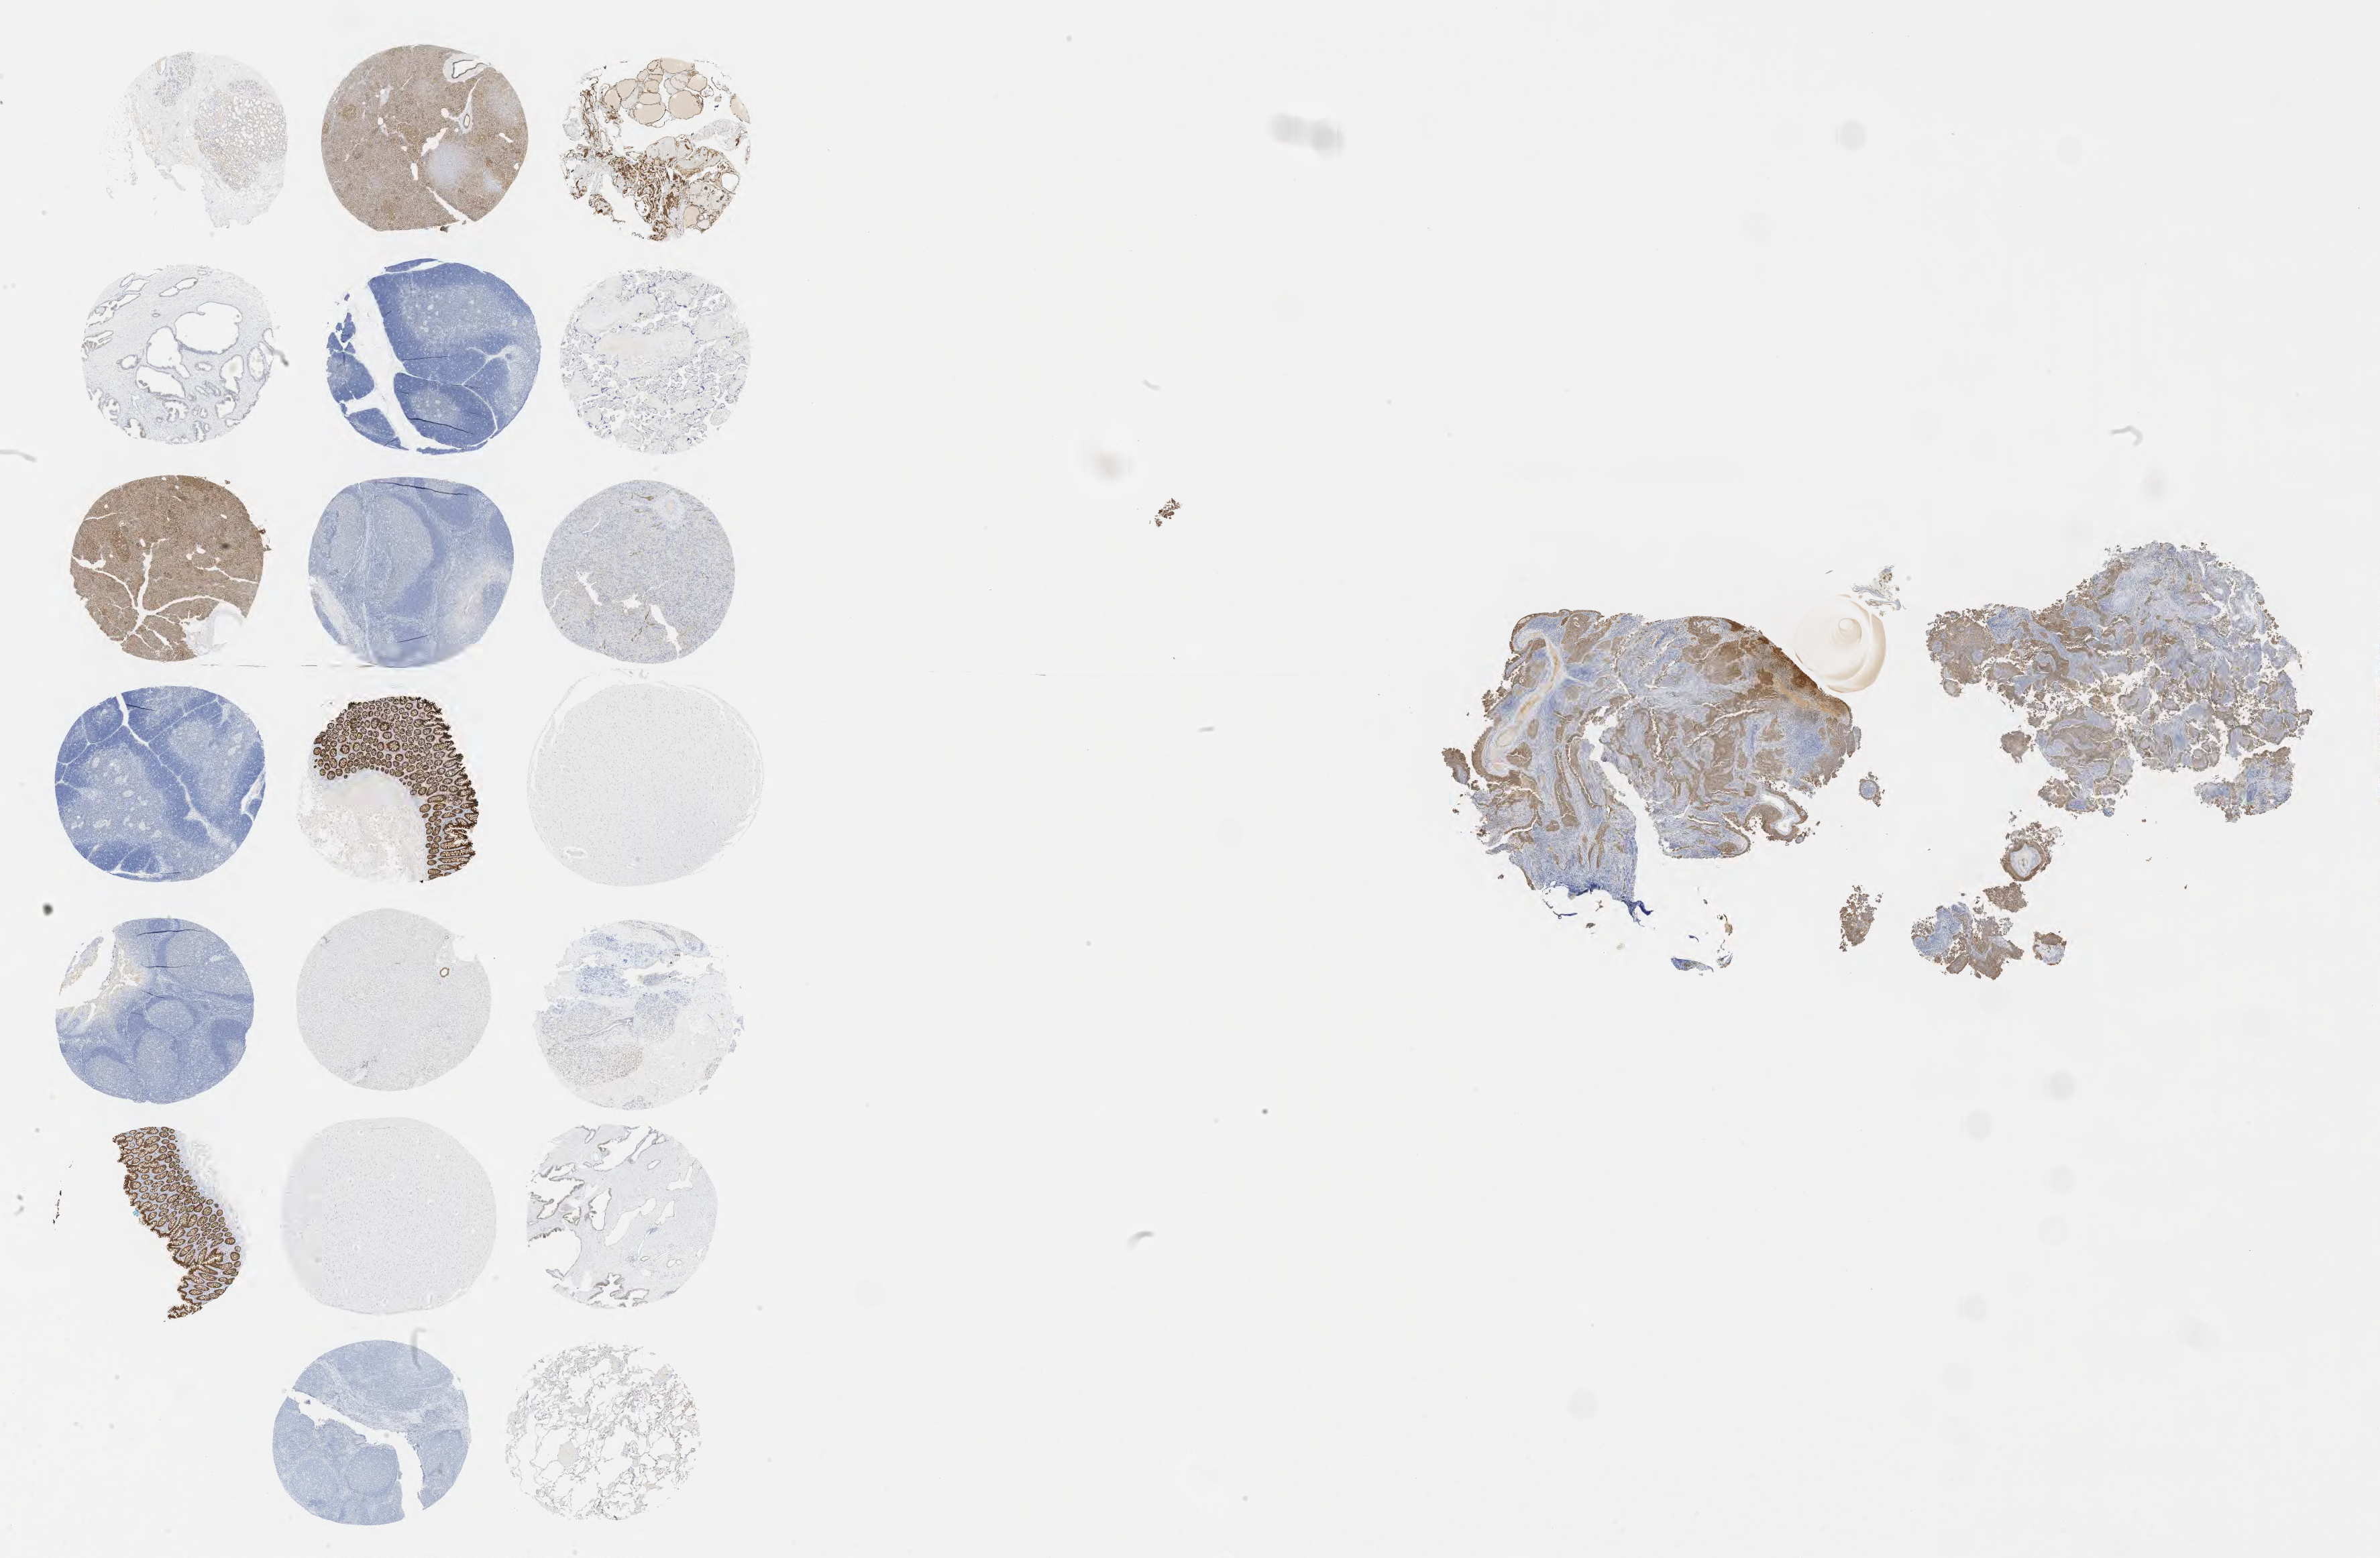
IHC for Ber-EP4, whole-slide image, a low-resolution overview of the entire scanned area, about 28.7 x 18.8 mm. Specimen: tumor tissue. Site: cervix. Patient: female, aged 65.
Histologic diagnosis: Squamous cell carcinoma, large cell, nonkeratinizing, NOS.